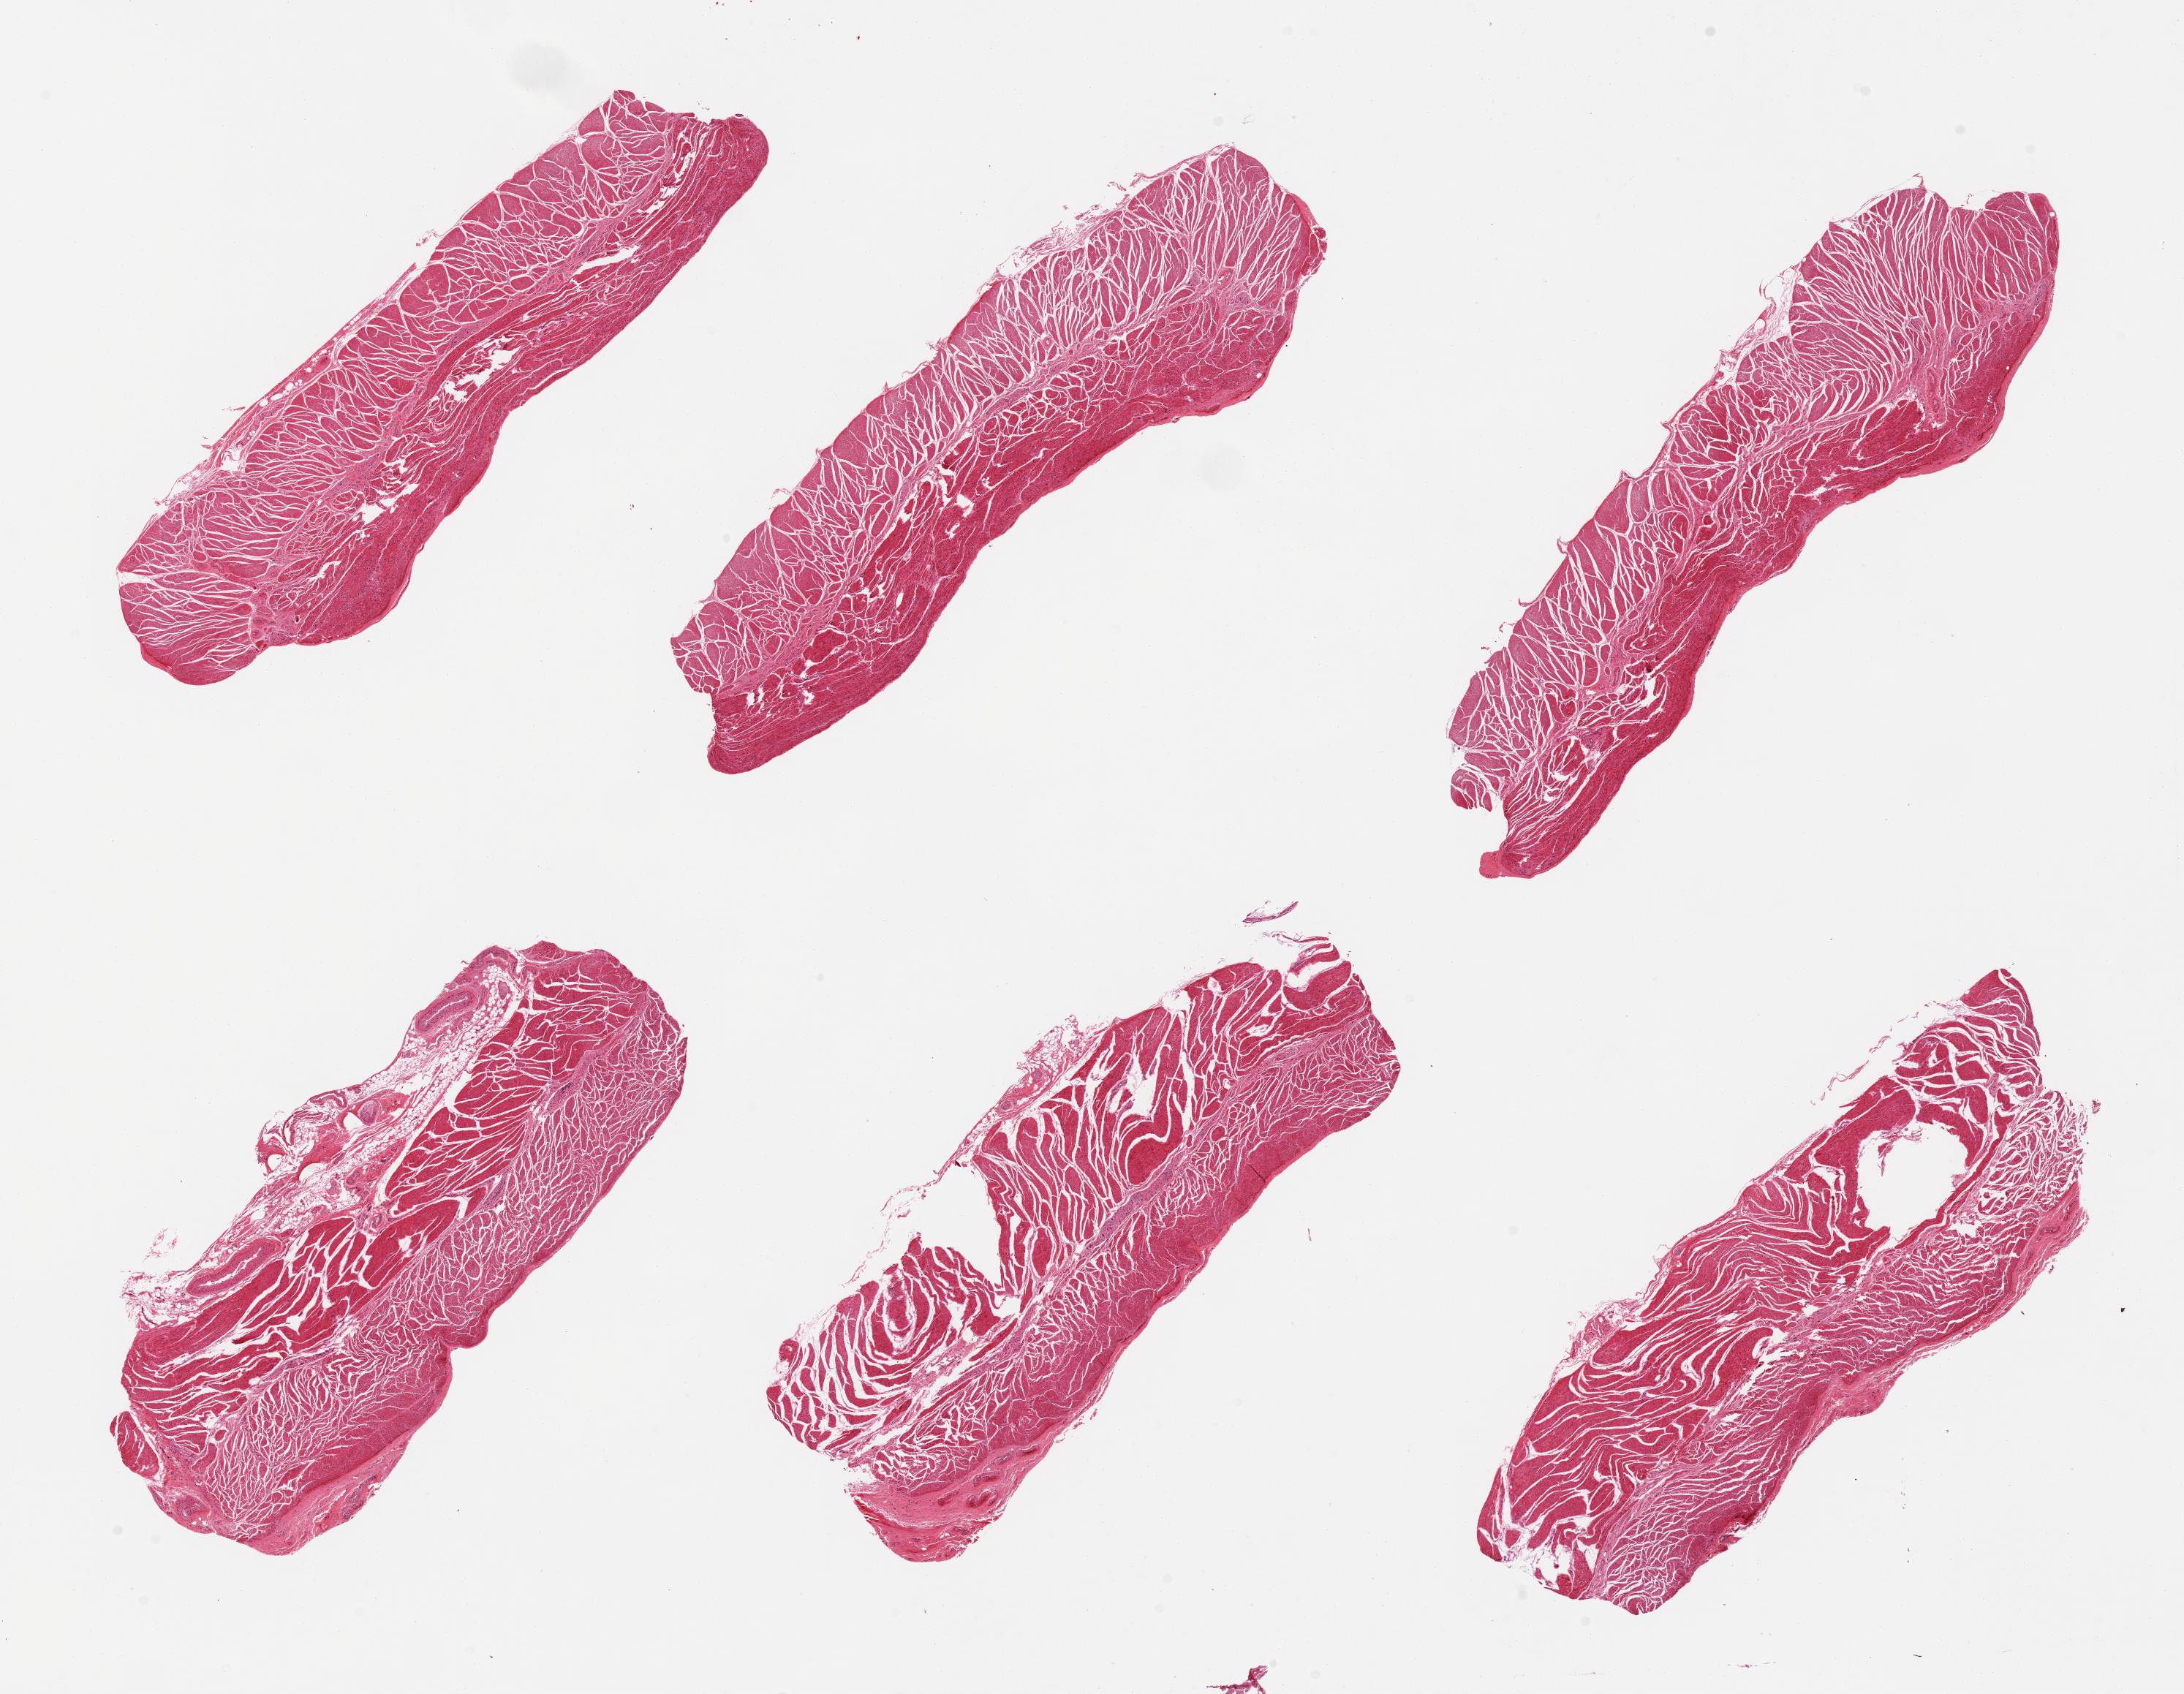
Whole-slide image, H&E stain — shown as a low-resolution overview of the whole scanned area (about 23.6 x 18.3 mm). PAXgene-fixed, paraffin-embedded tissue. Sampled site (target tissue): esophageal muscle. Tissue donor sample. Donor: male.
Reviewer comment on this tissue sample: 6 pieces, all muscularis, good specimens.